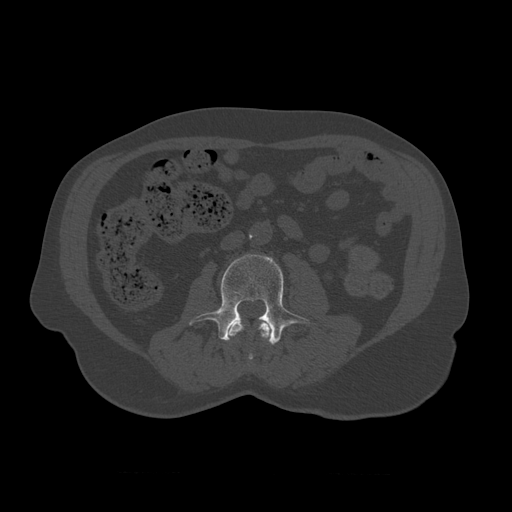
CT including the spine, one axial slice. Position 308 of 450 along the scan axis. Bone window (W 1800 / L 400 HU). 1.25 mm slice thickness. 512 × 512 image matrix, field of view 405 × 405 mm. Patient age 75 years. From the clinical record (not read from this slice): primary cancer: prostate.
Outlined on this slice (semi-automatic segmentation, software-assisted and operator-edited):
- L2 vertebra: box from (x=229, y=320) to (x=272, y=361) px
- L3 vertebra: (x=189, y=254)–(x=310, y=345)